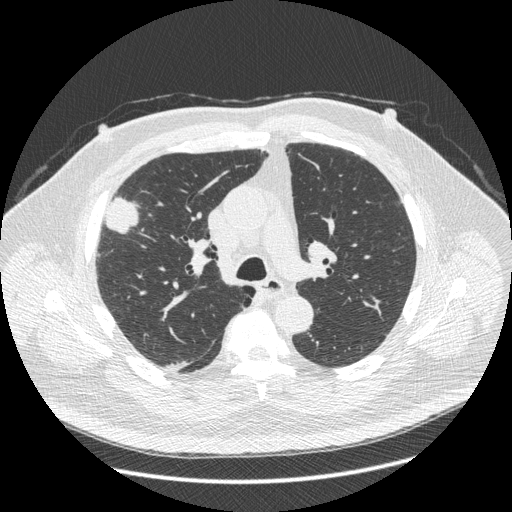
Low-dose screening chest CT, axial slice, third screening round (two years after baseline), lung window (W 1500 / L -600 HU), 1.25 mm slice thickness. Male, age 66 years at enrolment. Current smoker at enrolment.
• Lesion marked by an expert reader, bounding box [x1, y1, x2, y2] px = [86, 184, 145, 265].
• Screening reader's record for this exam (one nodule recorded; not confirmed to be the boxed lesion): non-calcified nodule or mass ≥4 mm, right upper lobe, 48 × 25 mm, spiculated (stellate) margins, soft tissue attenuation, pre-existing on the prior screen: no.